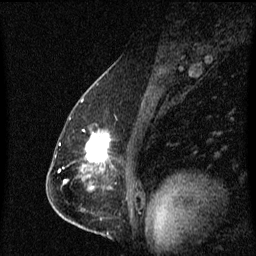
Breast MRI (dynamic contrast-enhanced), one sagittal slice. Slice 40 of 60 in the series (ordered by position). Dynamic contrast-enhanced series, image 2 of 3 at this slice position (ordered by acquisition). 1.5 T. TE 4.2 ms, TR 8.4 ms. 2 mm slice thickness. 256 × 256 image matrix, field of view 200 × 200 mm. Female patient, age 57 years. Case-level facts recorded for this patient, not image findings: setting: breast cancer imaged before/during neoadjuvant chemotherapy; receptor status: HR-positive, HER2-negative.
Structures marked on this image (semi-automatic segmentation, software-assisted and operator-edited):
- analysis volume of interest (the breast-tissue region the enhancement analysis was run in; not a lesion): bounding box [x1, y1, x2, y2] px = [83, 128, 113, 177]
- tumour enhancement mask (voxels above the 70 % enhancement threshold inside the analysis volume of interest): [86, 134, 110, 163]